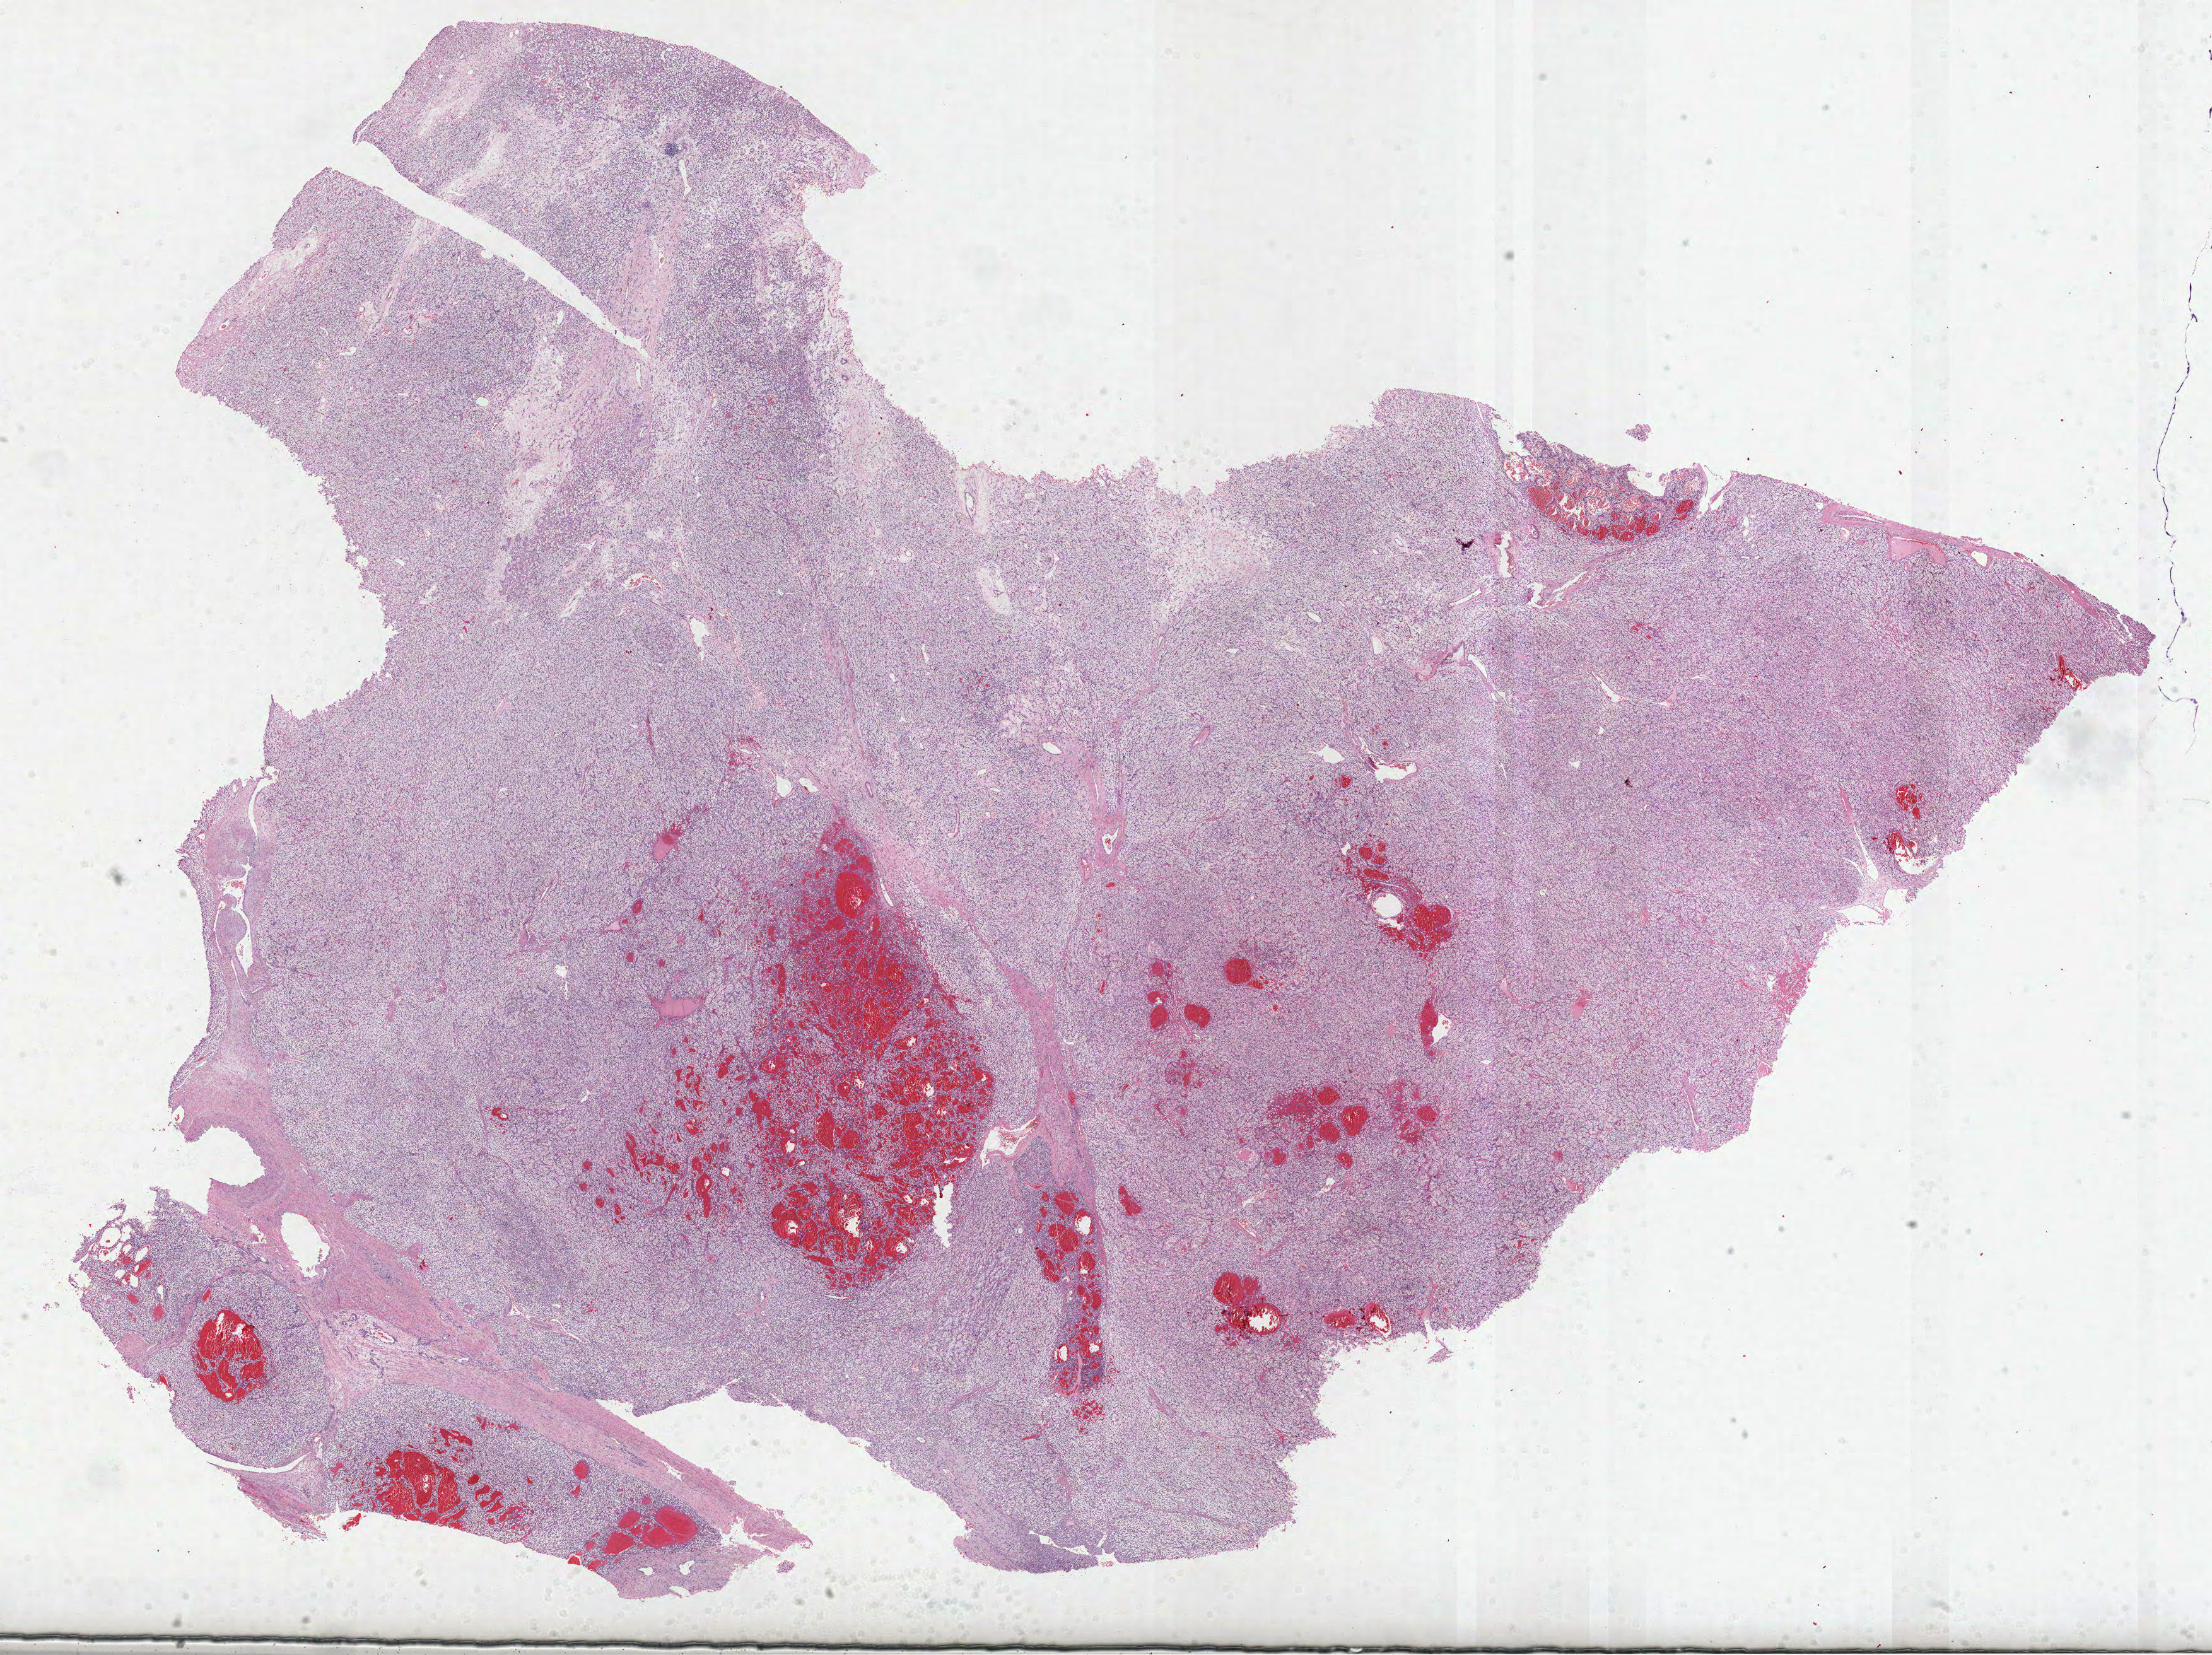
Hematoxylin and eosin (H&E) stained whole-slide image, a low-resolution overview of the entire scanned area, about 28.3 x 21.2 mm, formalin-fixed paraffin-embedded (FFPE) diagnostic section, kidney, primary tumour sample. Male patient; age at initial diagnosis 63 years. Histologic grade: G3 (poorly differentiated).
Histologic diagnosis: Clear cell adenocarcinoma, NOS. Laterality: left. AJCC pathologic stage: I.